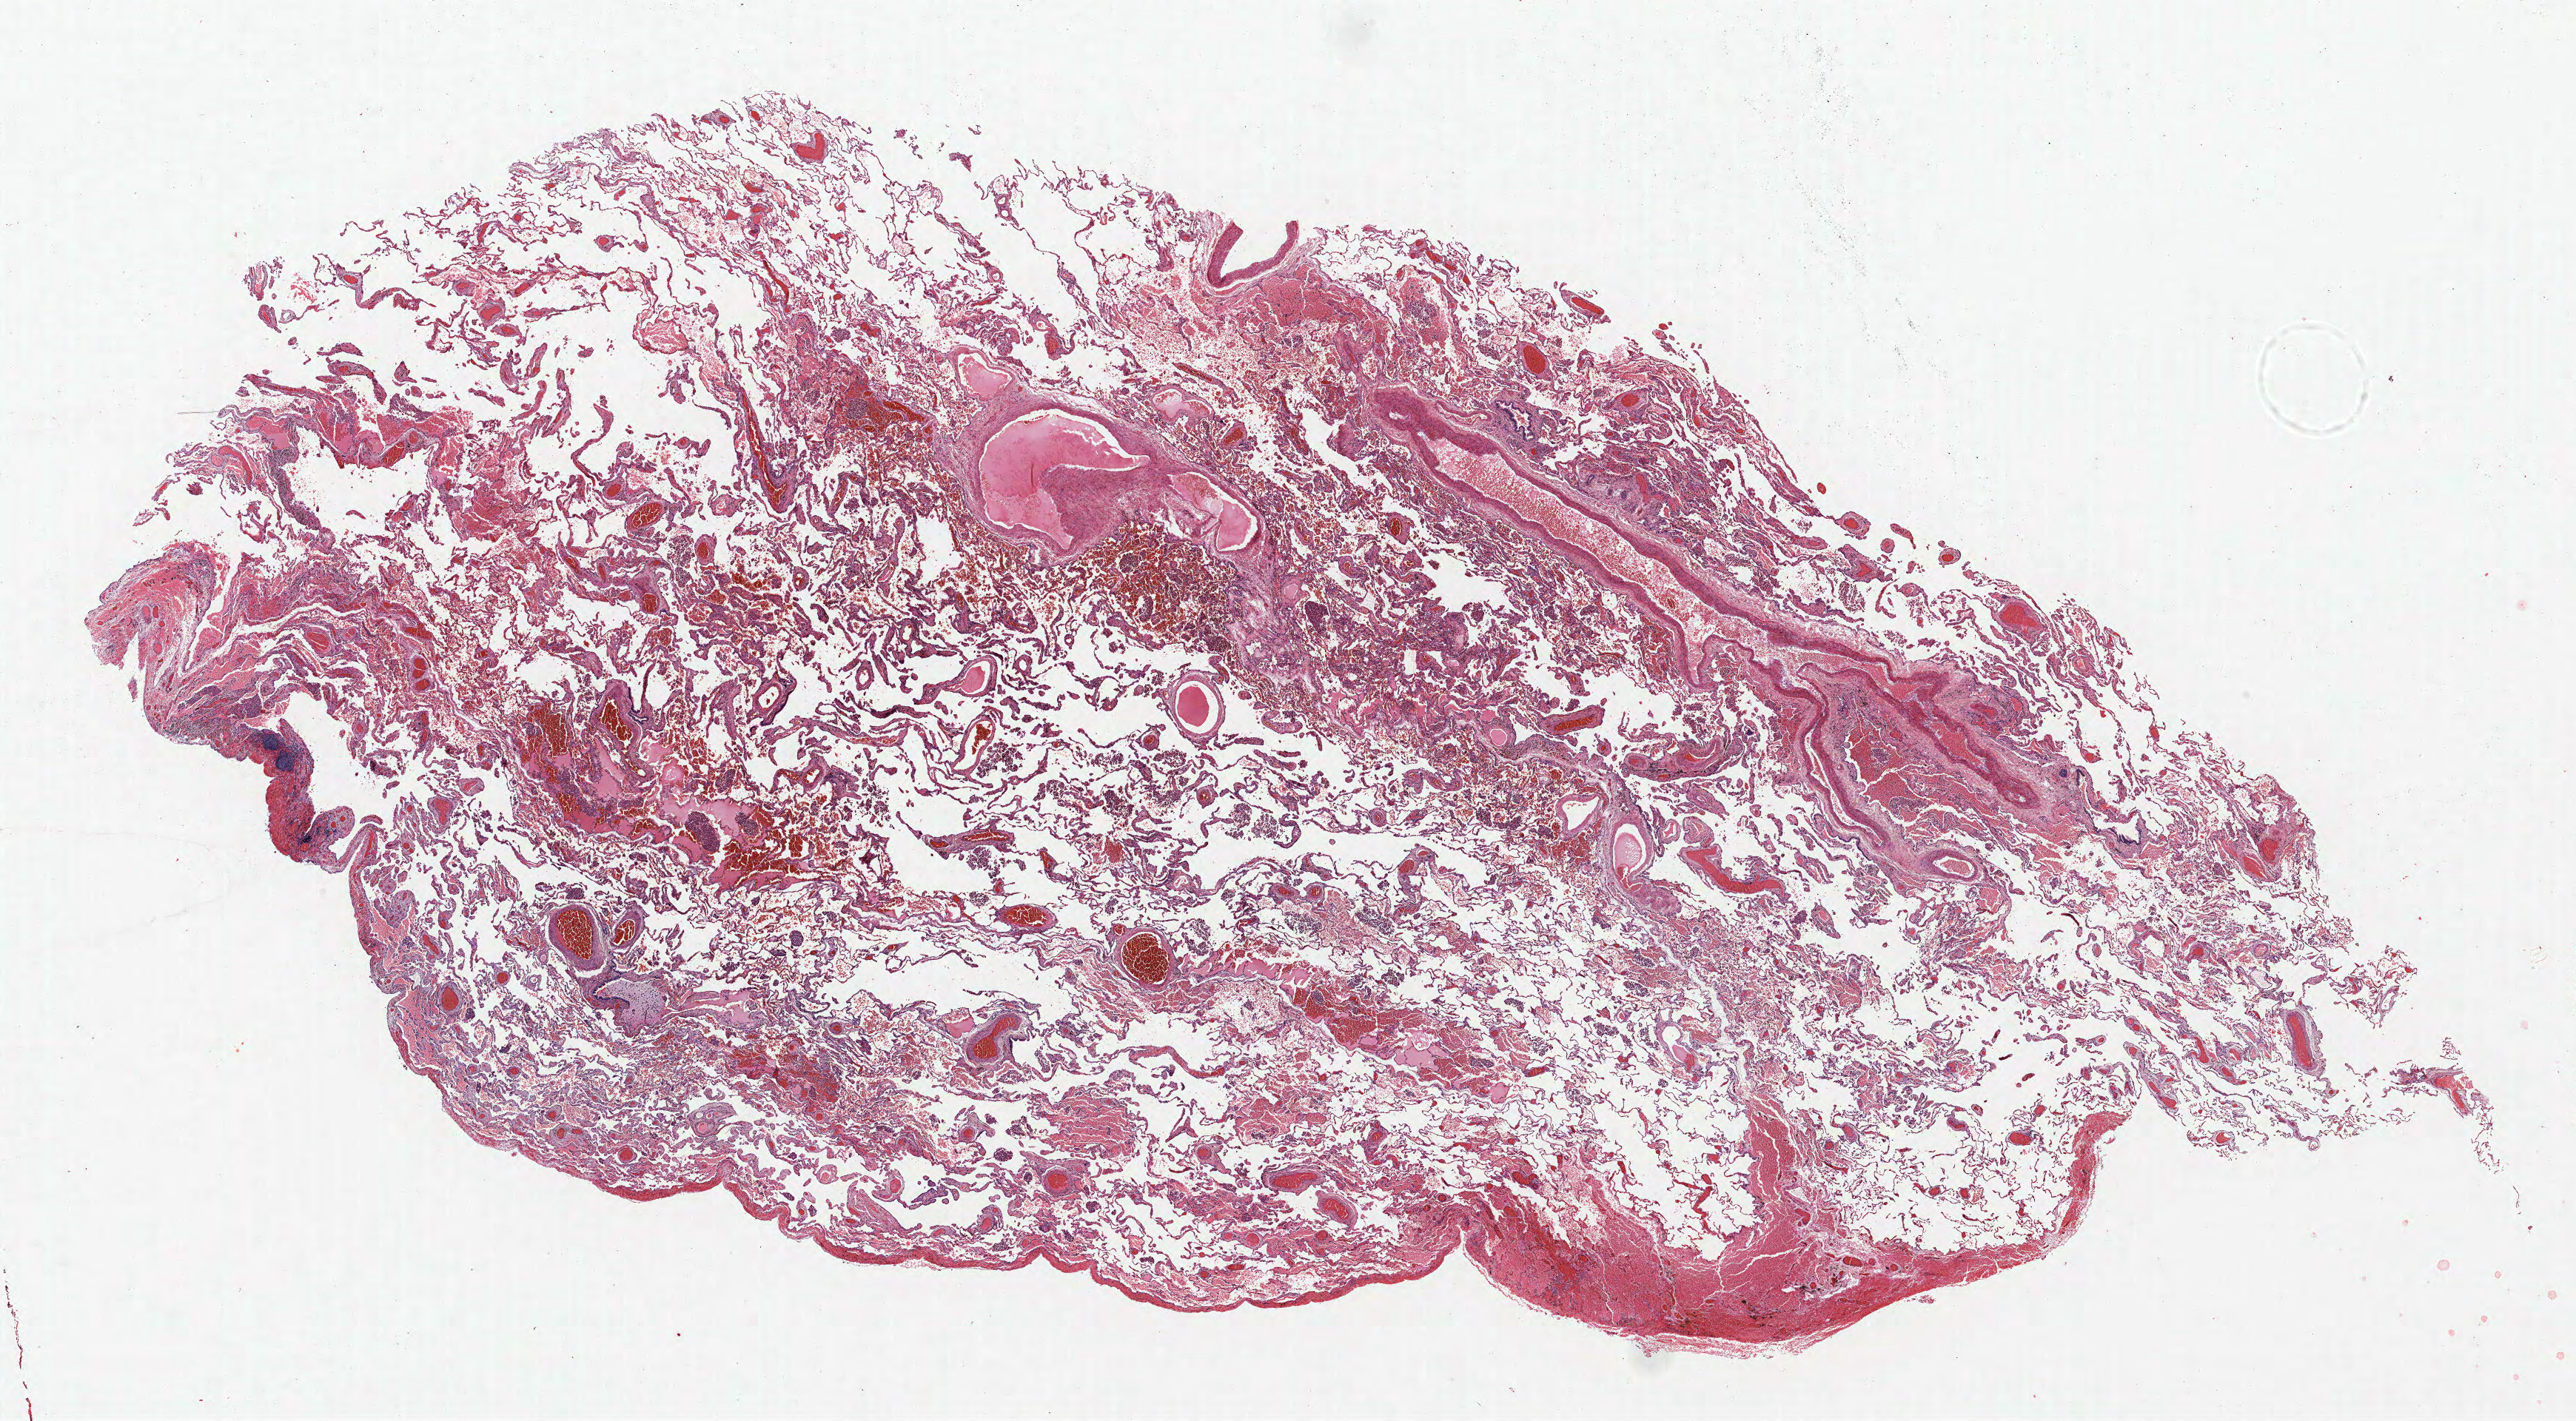
Whole-slide histology image, H&E, shown as a low-resolution overview of the whole scanned area (about 27.8 x 15.4 mm, slide scanned at 40x), FFPE section, lung tissue. Male, age 59 at enrolment. Grade: poorly differentiated (G3).
ICD-O-3 topography: upper lobe of lung (C34.1). Primary tumour location (clinical record): left upper lobe. Tumour size (pathology): 9 mm. Participant's lung-cancer diagnosis: Squamous cell carcinoma, NOS (ICD-O-3 8070/3). Stage (AJCC 6th edition): IIA.